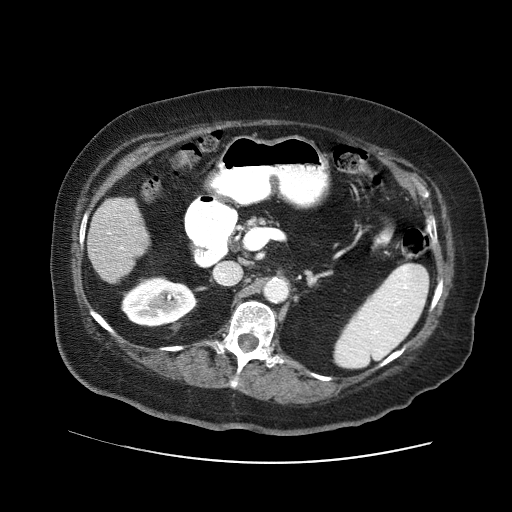
Contrast-enhanced abdominal CT (liver protocol), one axial slice. Position 16 of 71 along the scan axis. Reconstruction kernel STANDARD. Soft-tissue window (W 400 / L 40 HU). 2.5 mm slice thickness. 512 × 512 image matrix, field of view 400 × 400 mm. From the clinical record (not read from this slice): diagnosis: hepatocellular carcinoma (patient treated with transarterial chemoembolisation; whether this scan precedes or follows treatment is not stated here); TNM stage (as recorded): Stage-II; Child-Pugh class: A; tumour nodularity: multinodular; tumour size: 5 cm.
Structures marked on this image (semi-automatically segmented with operator editing):
- liver parenchyma outside the tumour (the mass and vessels are separate outlines, so this box may not span the whole liver): bounding box (x1, y1, x2, y2) in pixels: (88, 198, 148, 282)
- liver vessels: (121, 247, 124, 250)